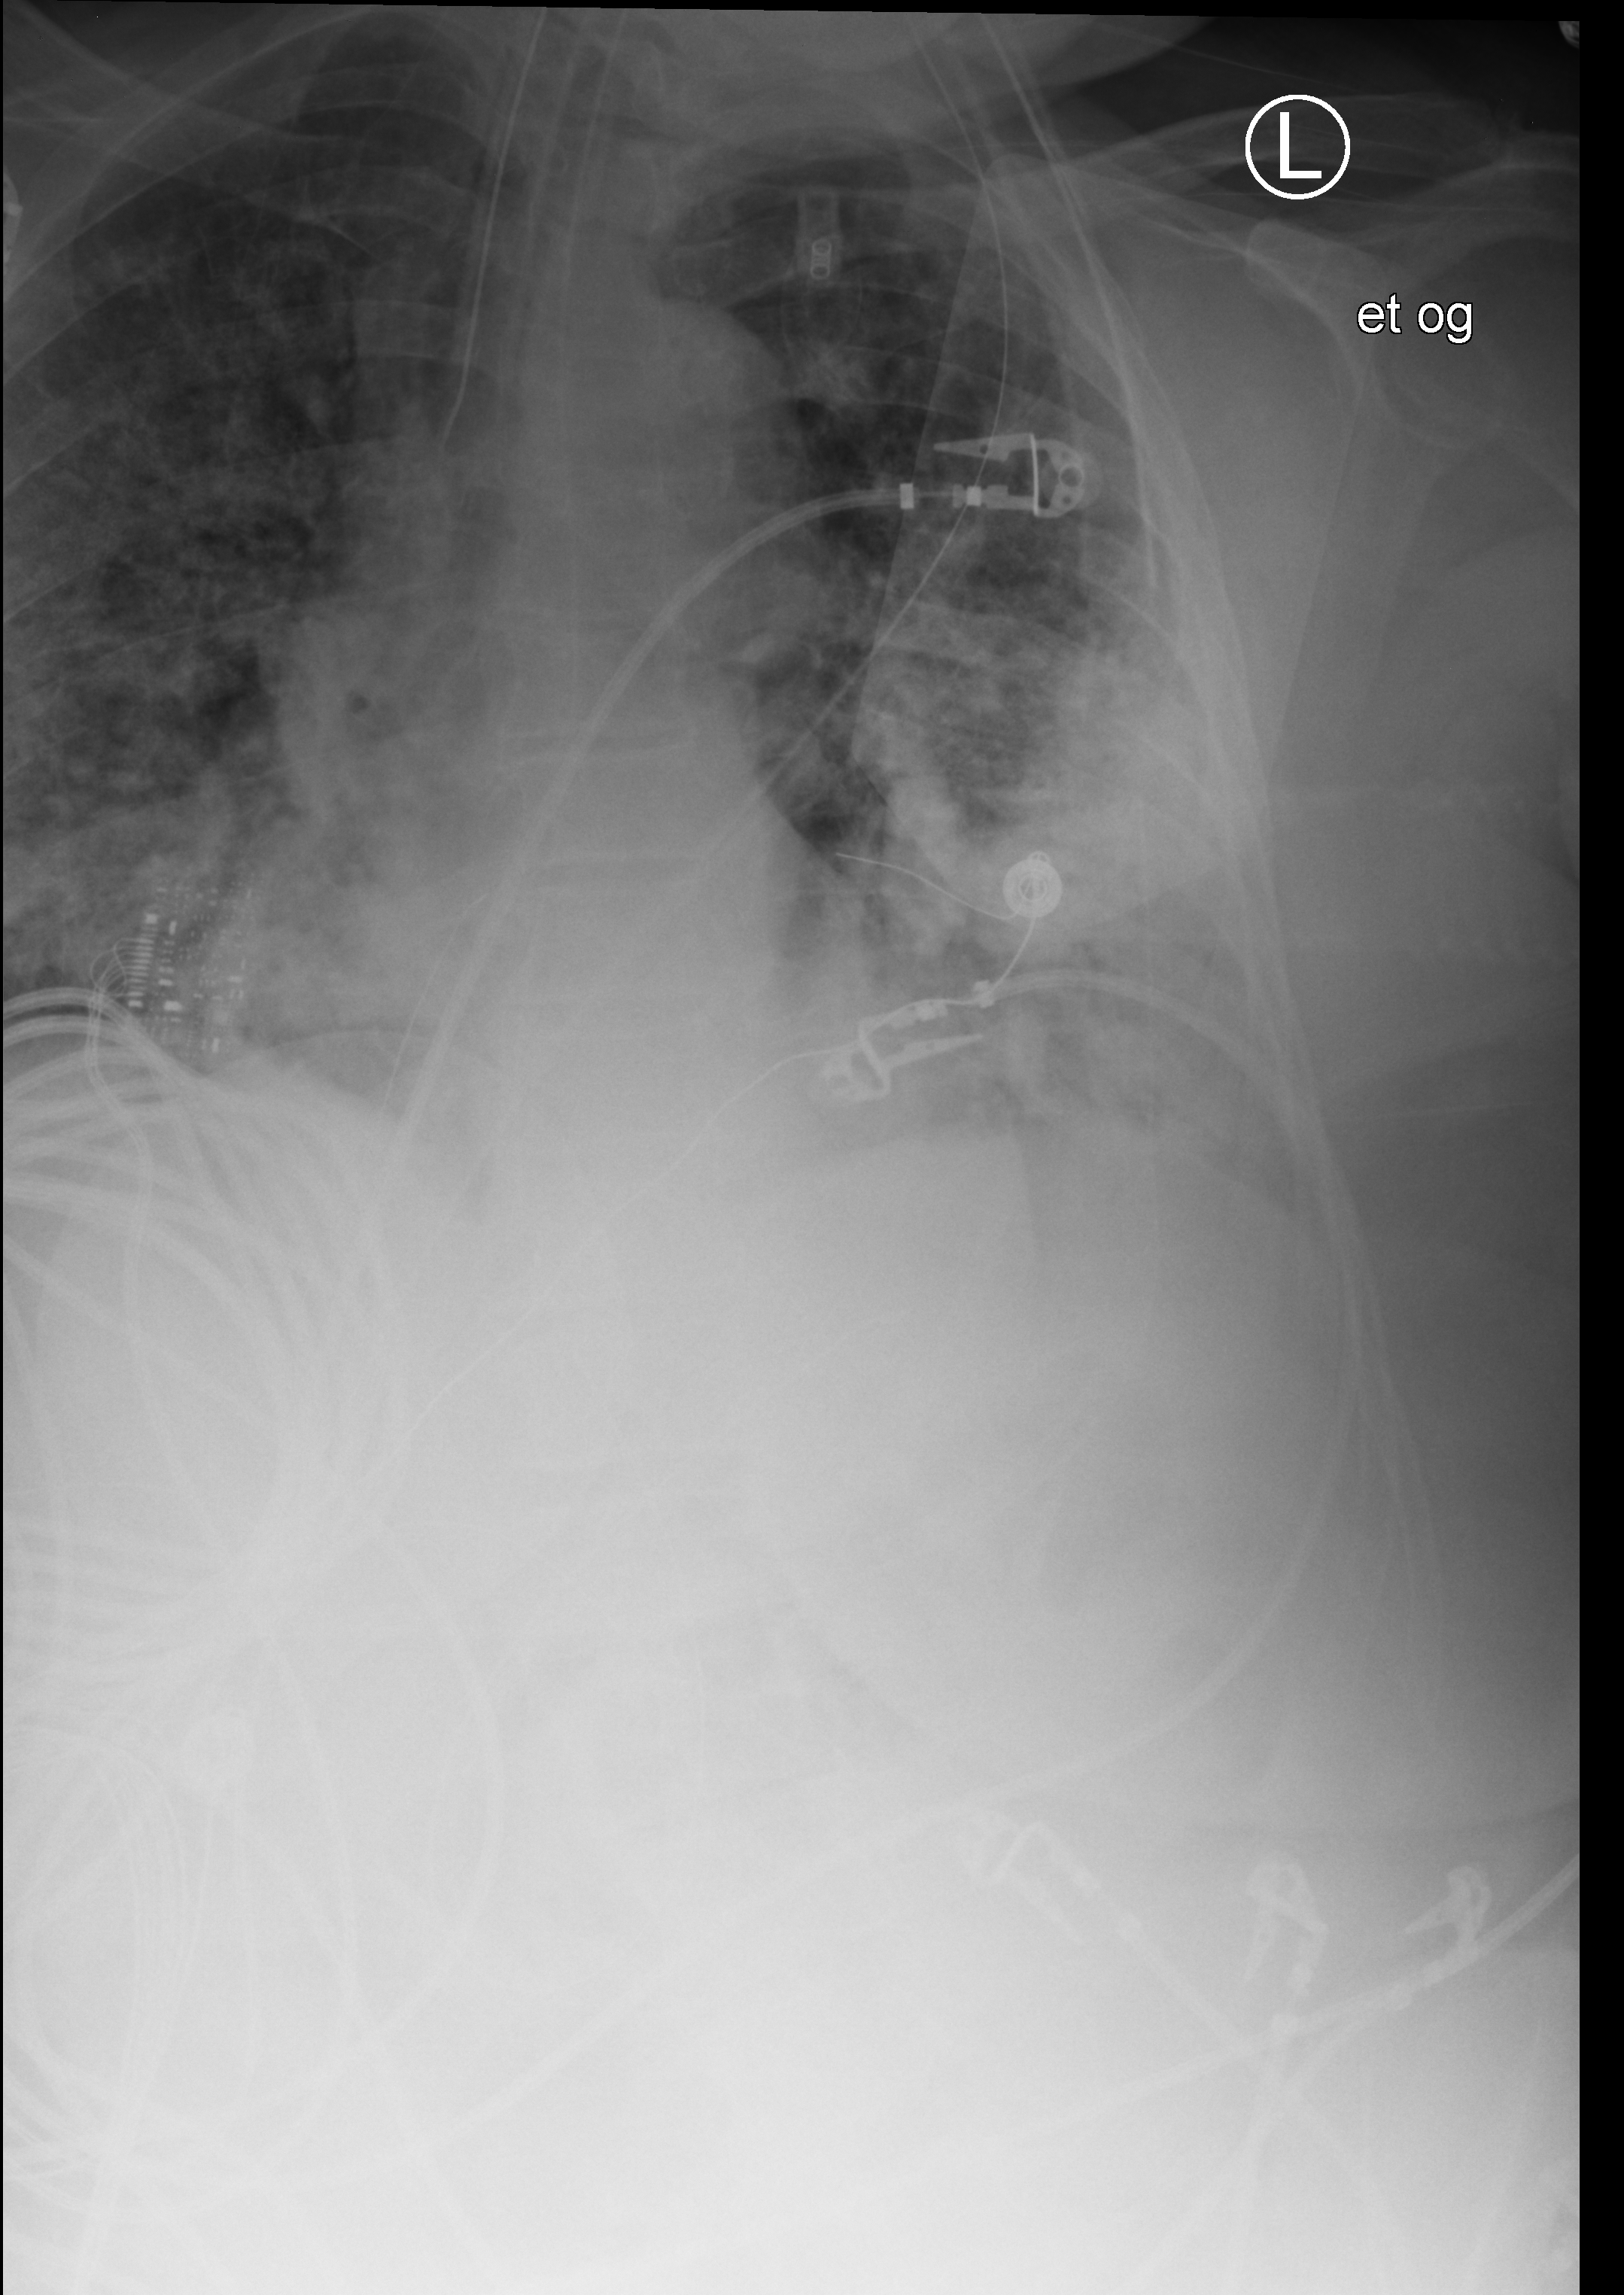
Portable chest radiograph, anteroposterior (AP) projection. Female patient hospitalised with COVID-19, age 60–74 years.
From the hospital-stay record, not from the radiograph (when in the stay this image was taken is not recorded): diabetes (admission record): no.